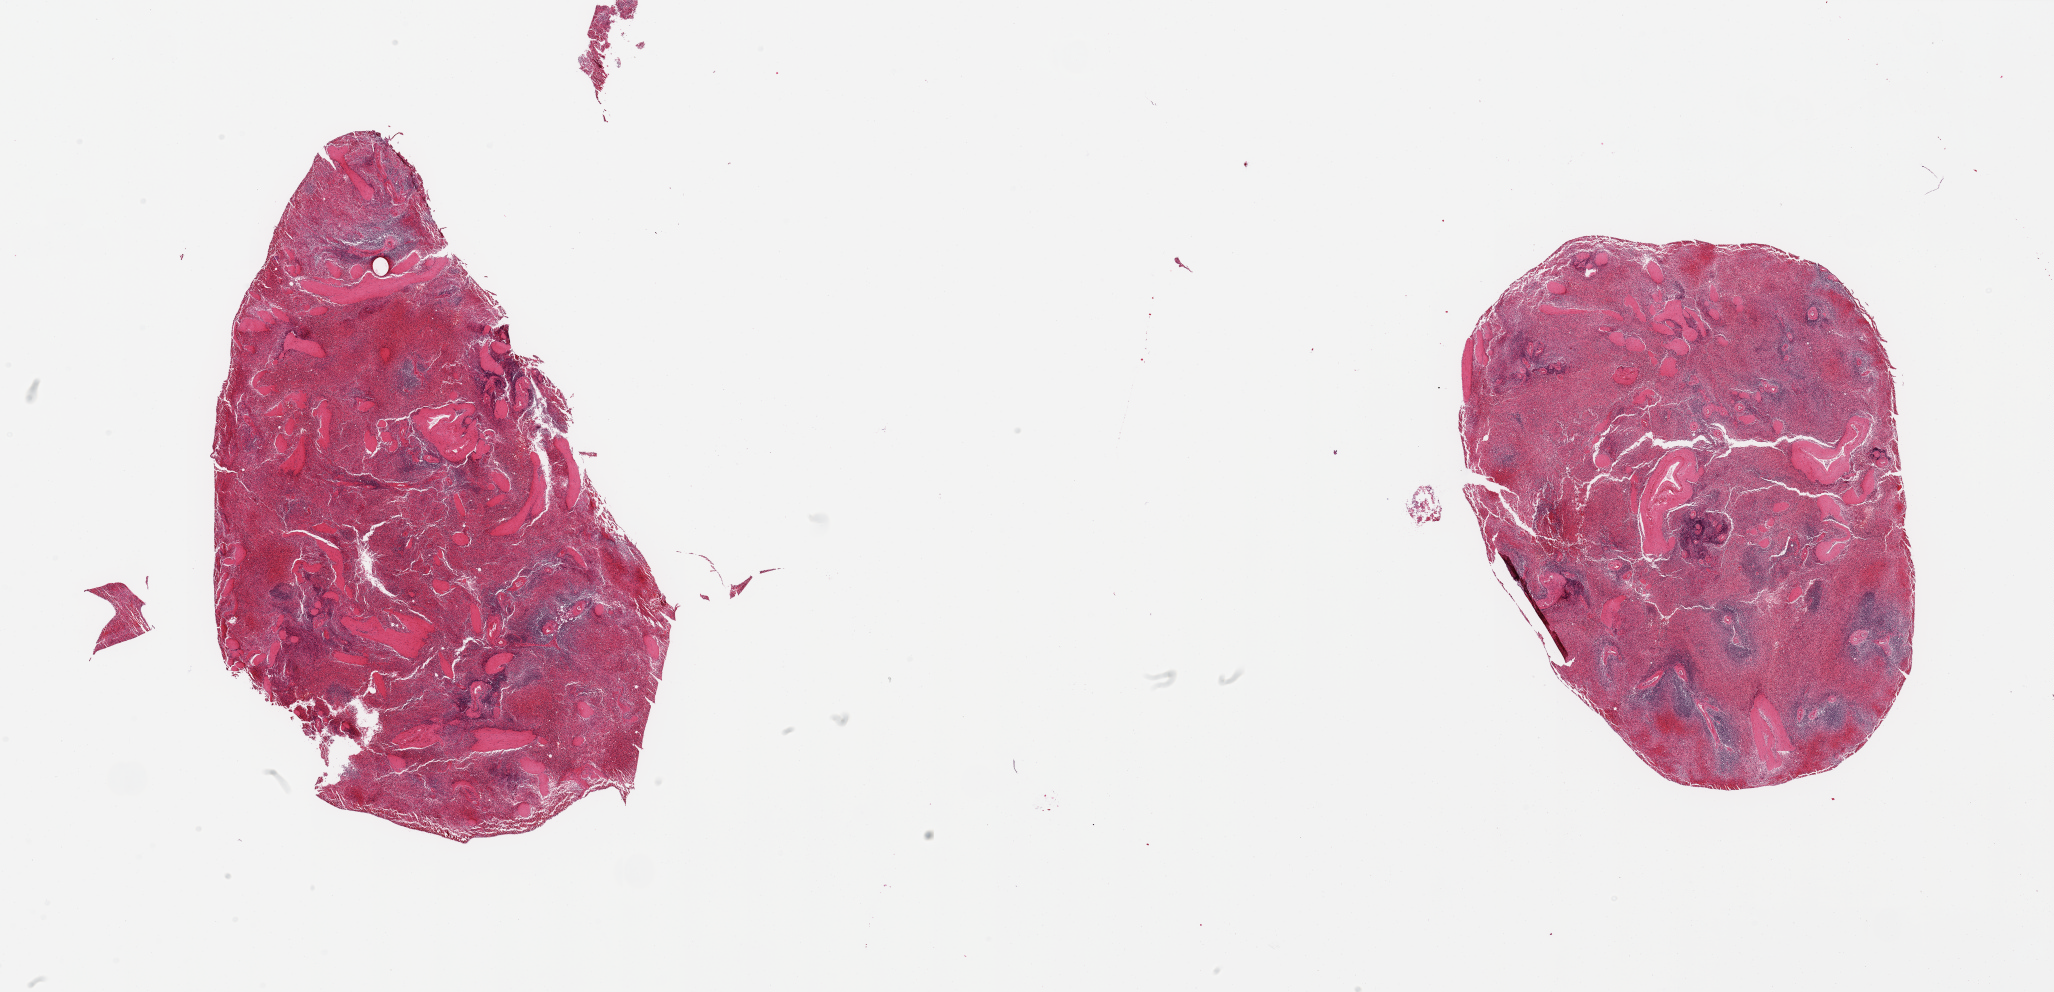
Whole-slide image, hematoxylin and eosin (H&E) stain, shown as a low-resolution overview of the whole scanned area (about 32.5 x 15.7 mm), PAXgene-fixed, paraffin-embedded tissue, section of spleen (target tissue), donor tissue sample. Donor: male.
- reviewer comment on this tissue sample: 2 partially fragmented pieces; moderately congested